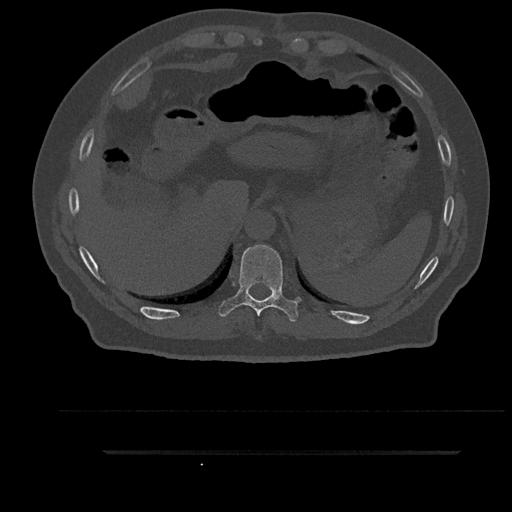
CT including the spine, one axial slice; position 369 of 797 along the scan axis; reconstruction kernel Br40s/3; bone window (W 1800 / L 400 HU); 0.5 mm slice thickness; 512 × 512 image matrix, field of view 432 × 432 mm. Patient: male, 63 years. Case-level facts recorded for this patient, not image findings: primary cancer: renal; vertebrae with lytic lesions (as recorded): T8.
Outlined on this slice (semi-automatically segmented with operator editing):
- T10 vertebra: box from (x=218, y=245) to (x=301, y=322) px